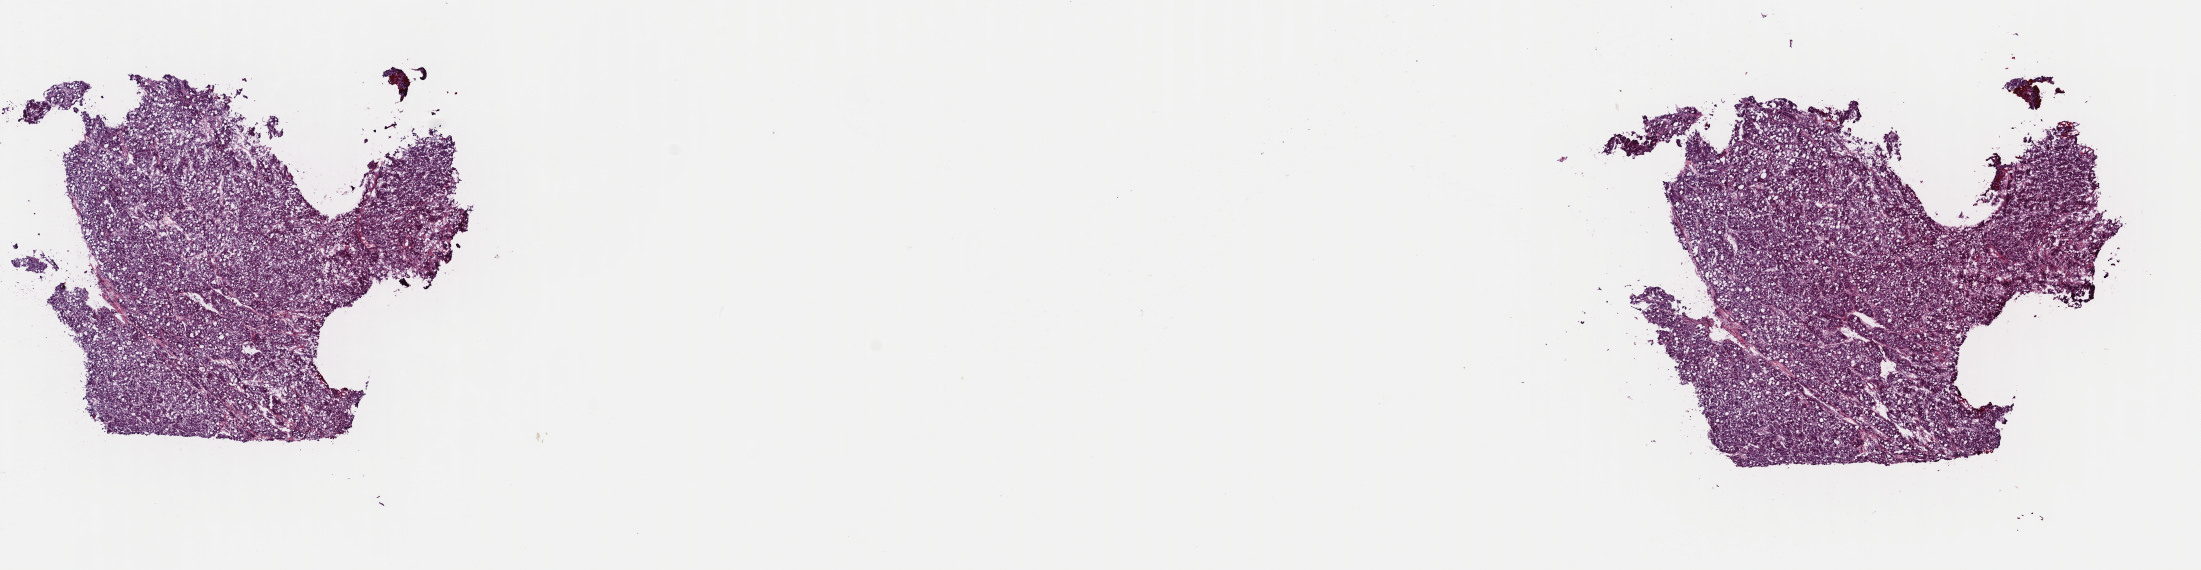
Digitized H&E tissue section (whole slide) — whole scanned area (about 17.4 x 4.5 mm) shown as a low-resolution overview. Frozen section from the top of the tissue portion. Primary tumour sample from the liver. Male patient; age at initial diagnosis 54 years.
Pathologic diagnosis: Hepatocellular carcinoma, NOS.